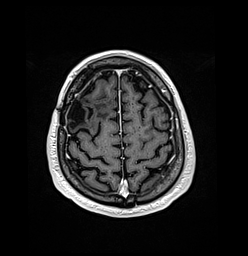
Brain MRI from a brain-tumour surgery series, one axial slice. Slice 35 of 176 in the series (ordered by position). T1-weighted post-contrast. 1 mm slice thickness. 248 × 256 image matrix, field of view 242 × 250 mm. Case-level facts recorded for this patient, not image findings: histopathology: Oligodendroglioma; WHO grade: 3; IDH mutation: yes; tumour location: Right Frontal.
Annotated regions visible in this slice (outlined manually by an expert reader):
- previous resection cavity: bounding box (x1, y1, x2, y2) in pixels: (69, 97, 86, 123)